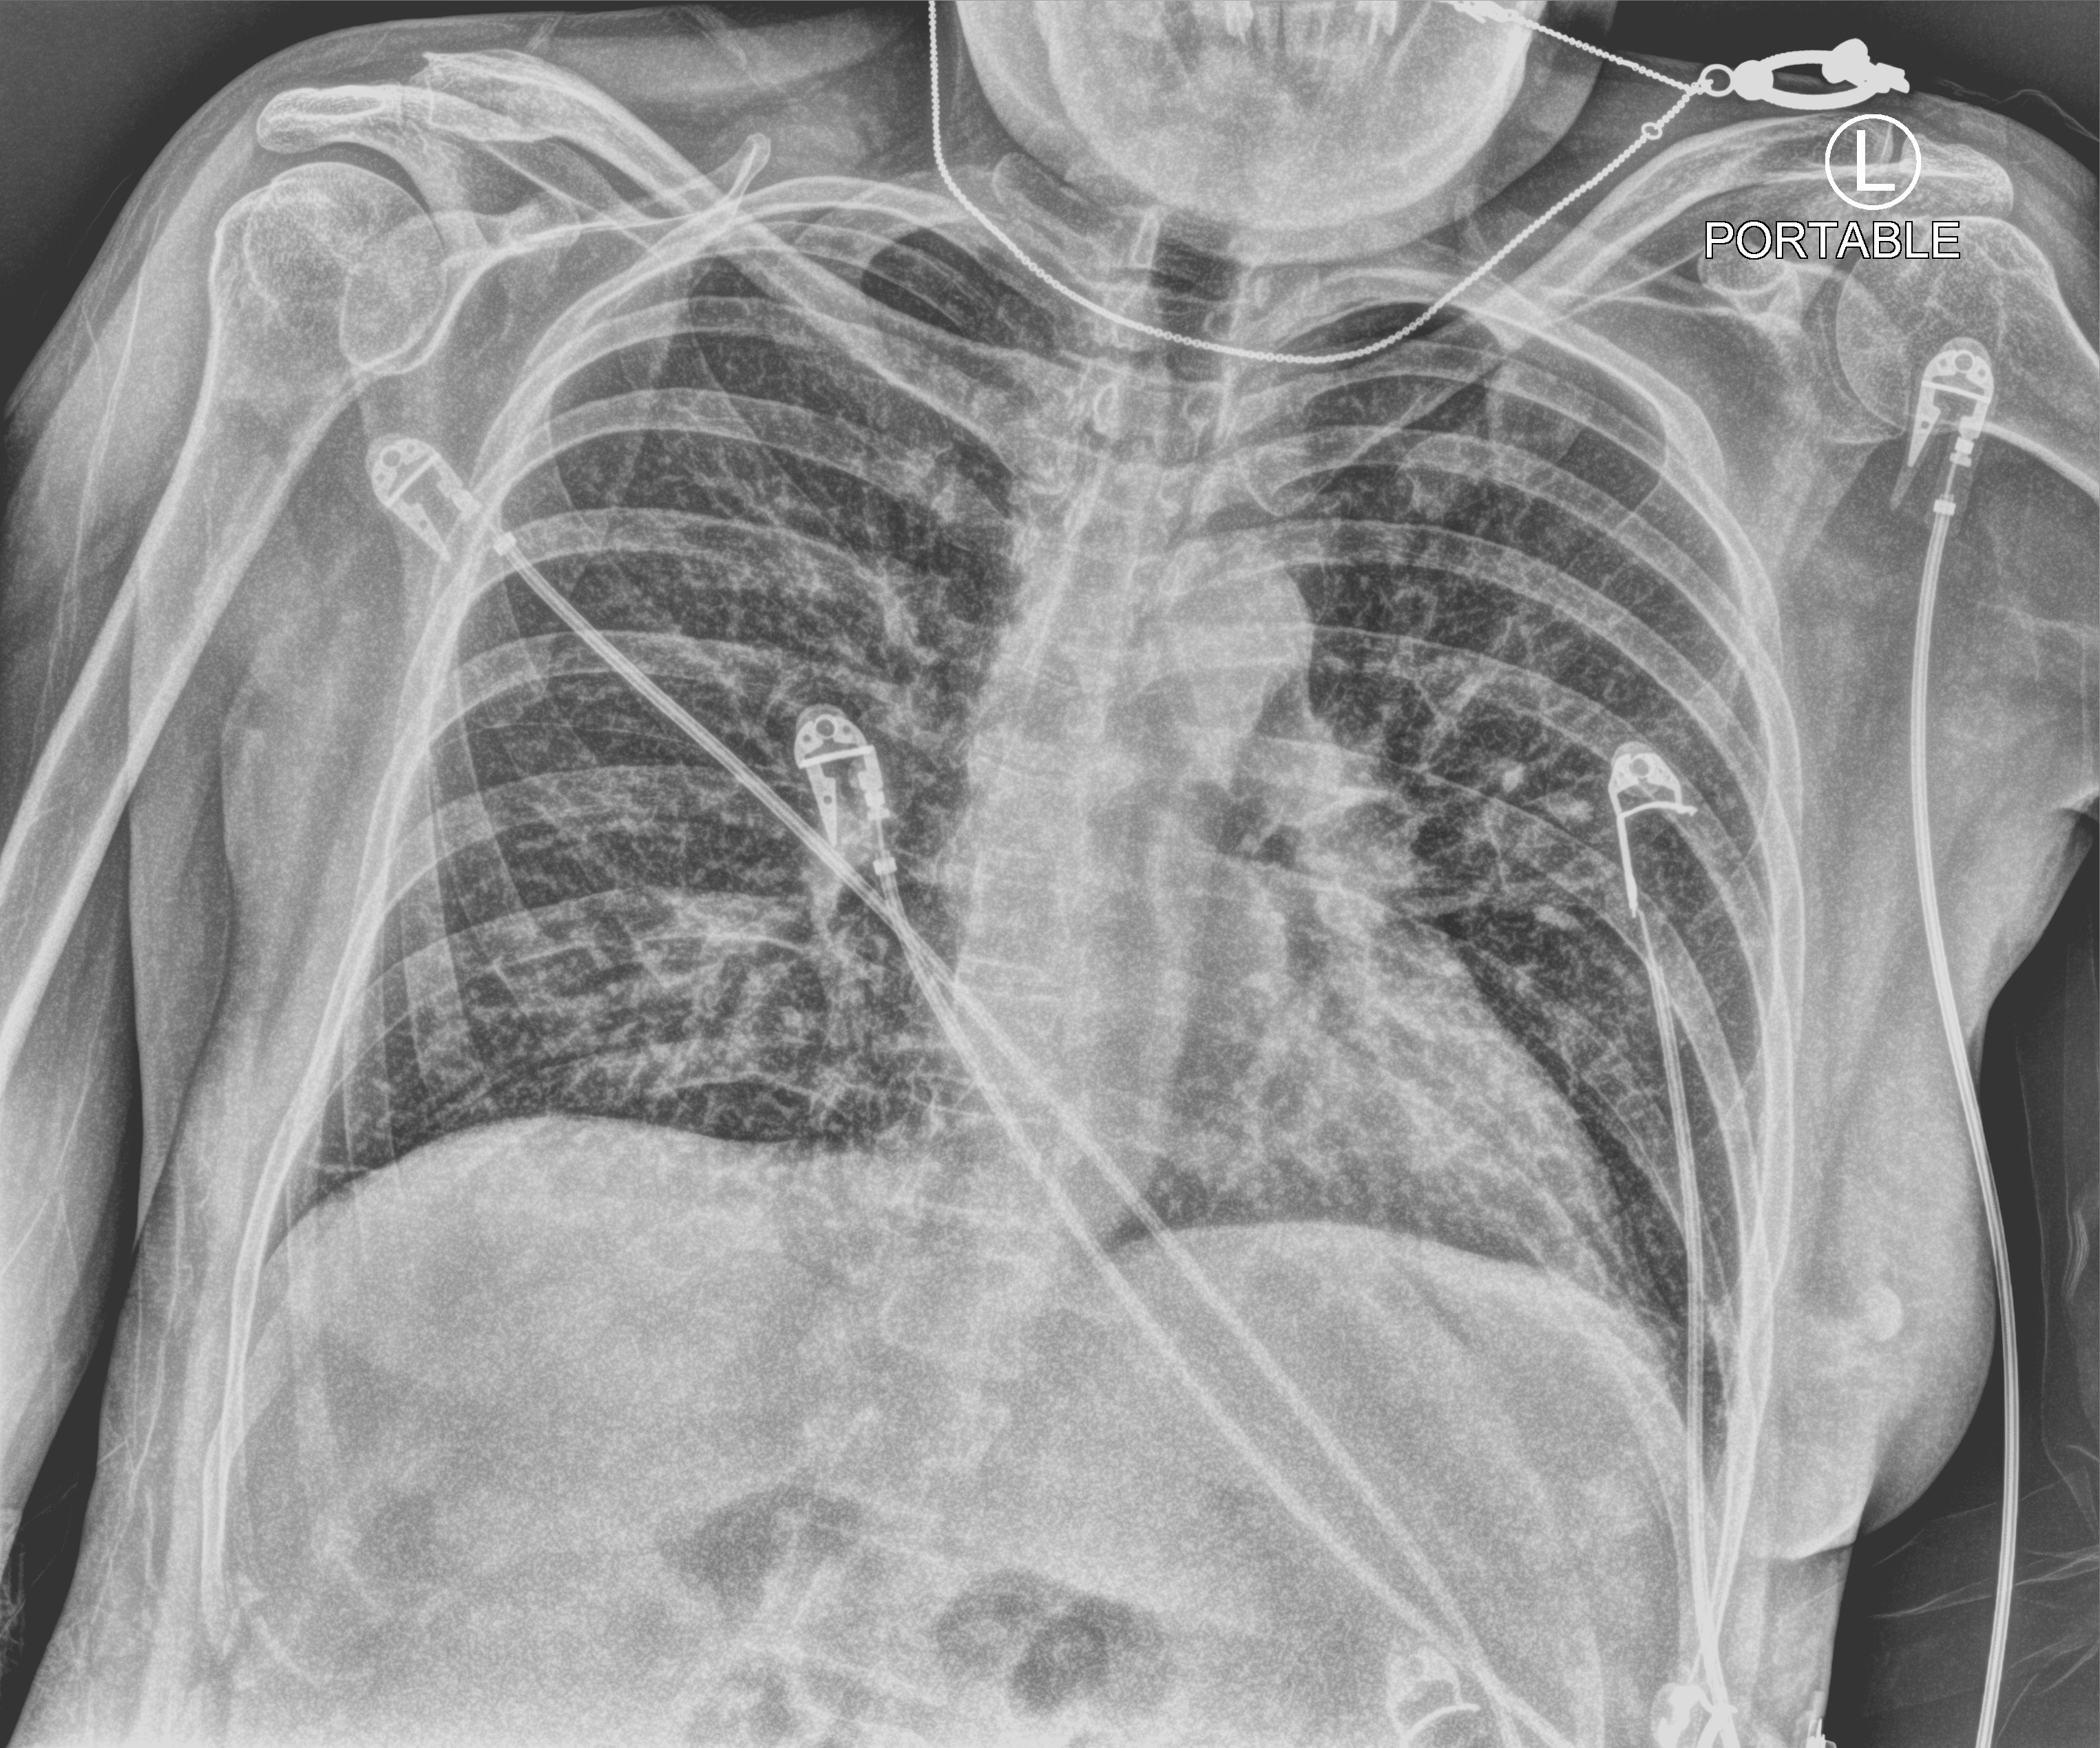
Bedside chest radiograph (computed radiography); anteroposterior (AP) projection. Patient hospitalised with COVID-19; female, aged 18–59 years.
From the hospital-stay record, not from the radiograph (when in the stay this image was taken is not recorded): diabetes (admission record): no.